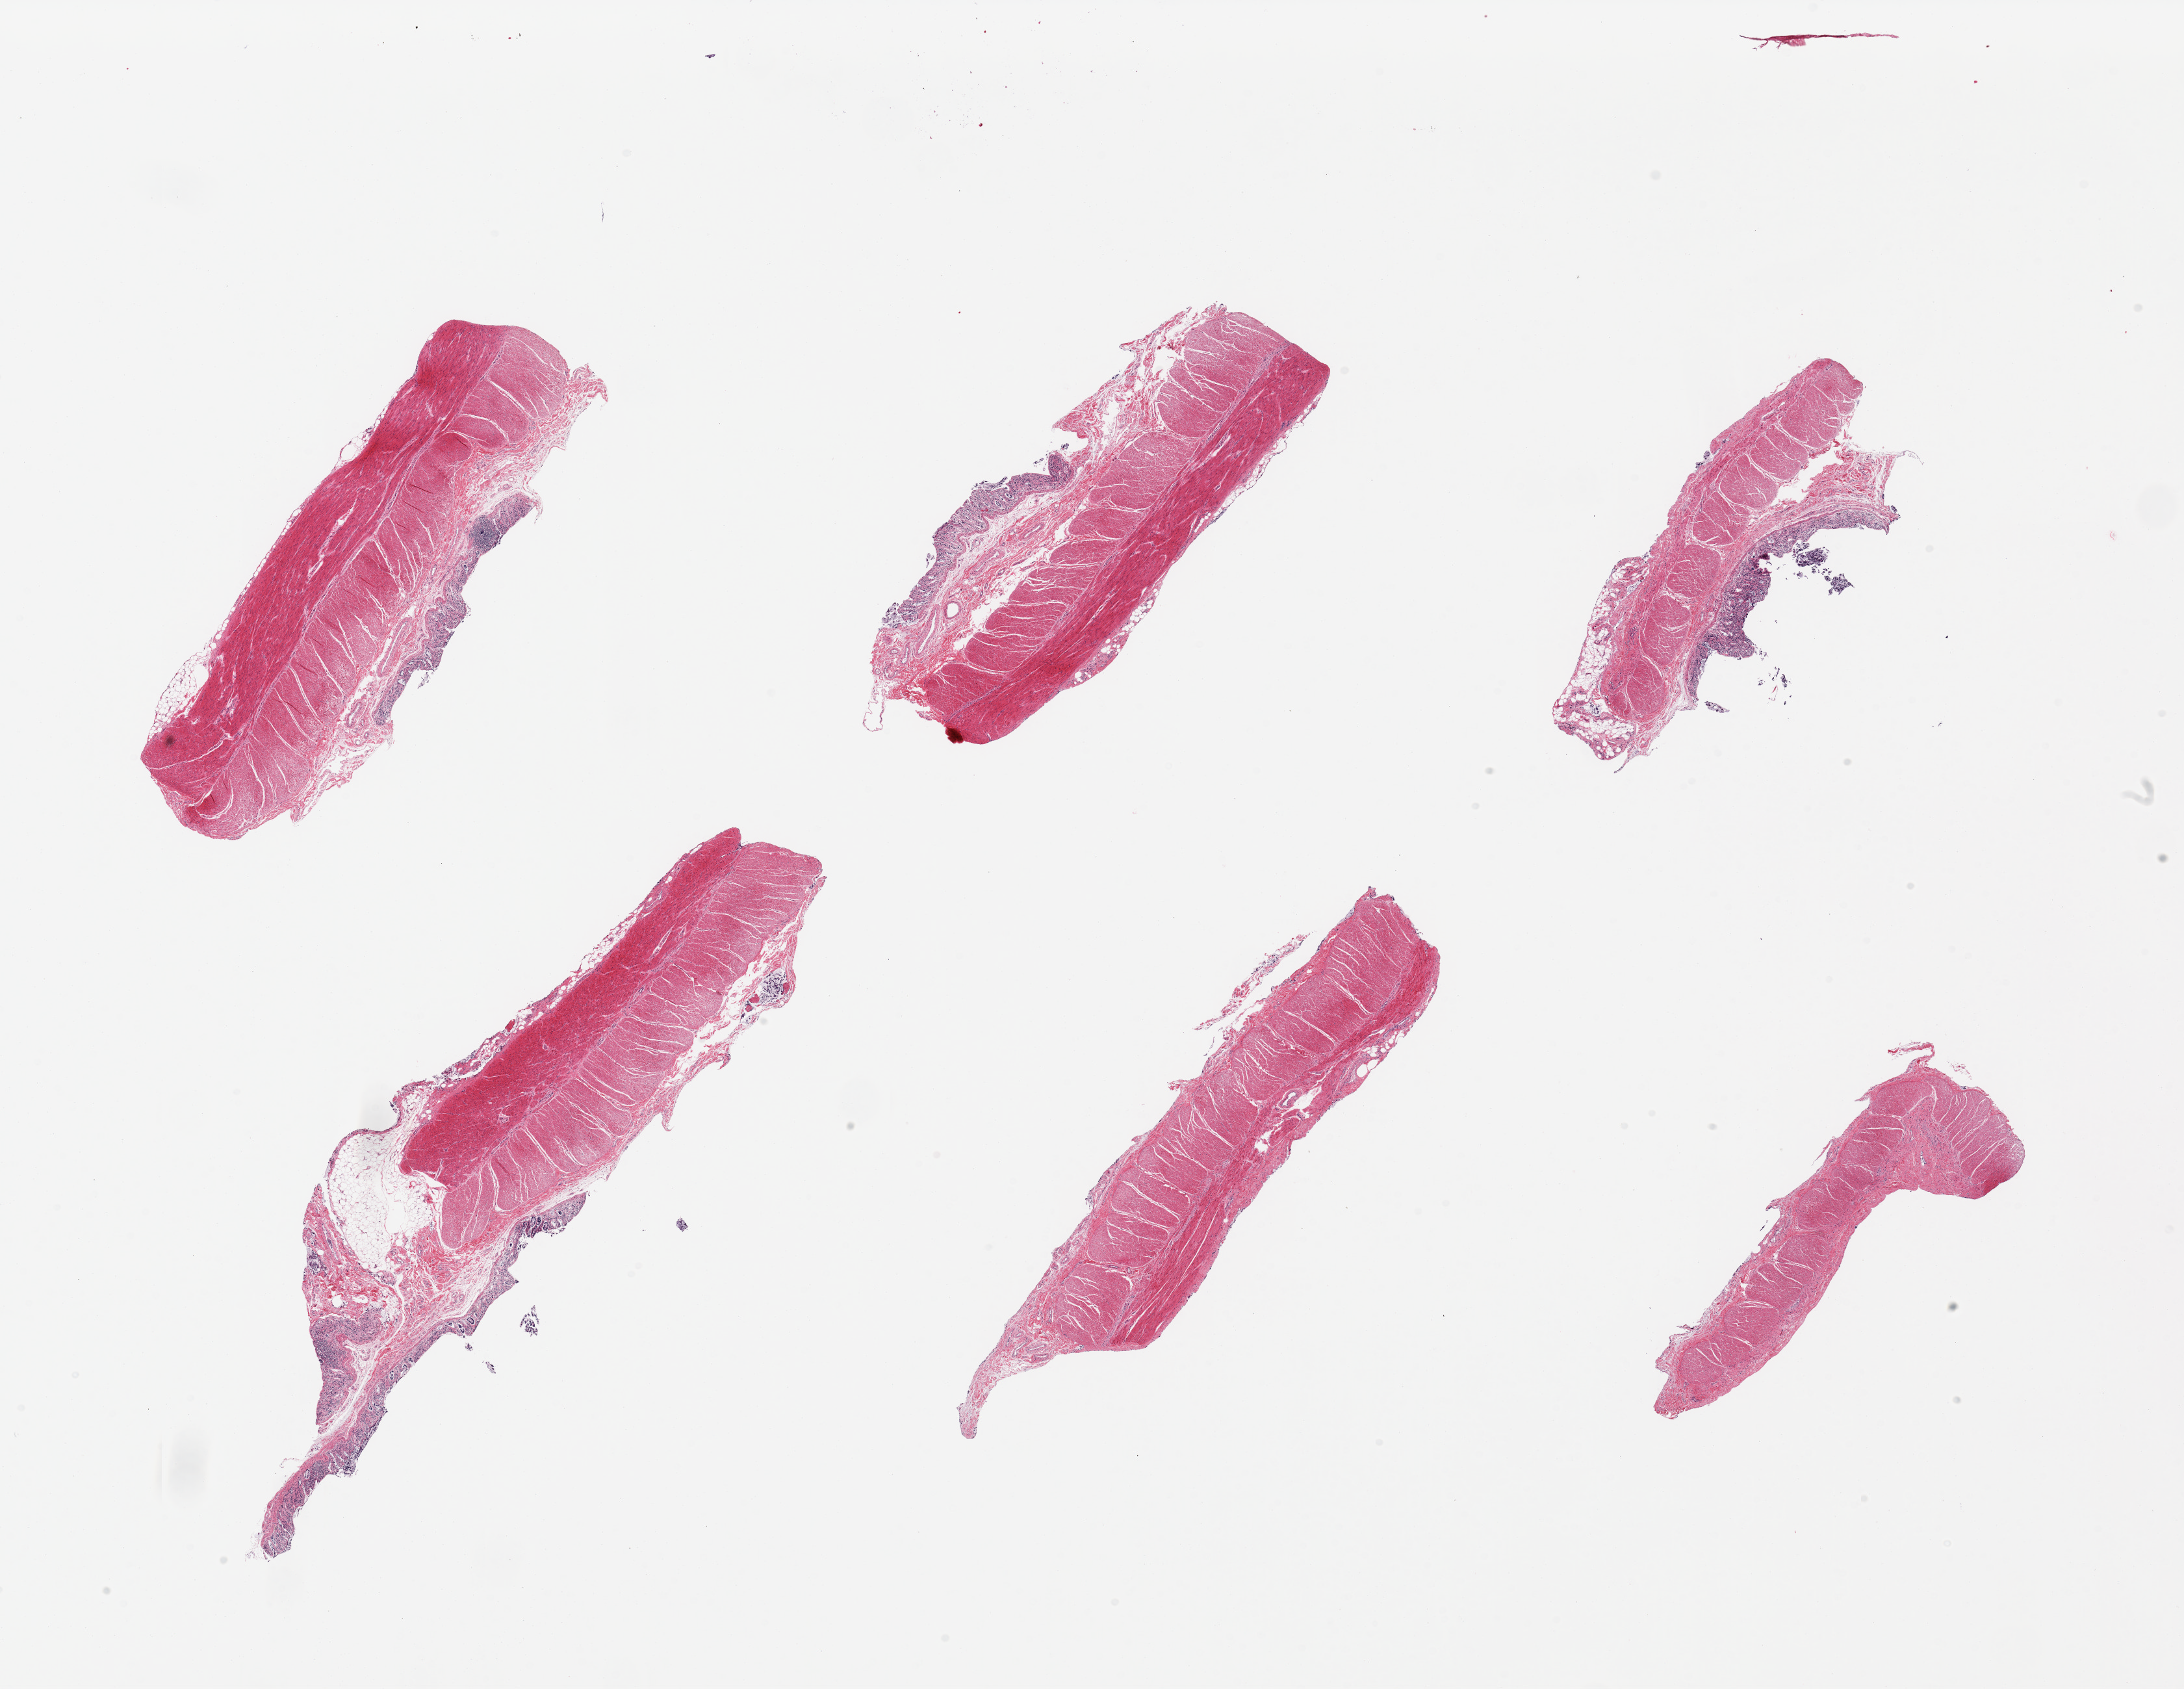
Digitized hematoxylin and eosin (H&E)-stained section, brightfield — whole scanned area (about 26.6 x 20.6 mm, slide scanned at 20x) shown as a low-resolution overview; PAXgene-fixed paraffin-embedded (PFPE) section; sampled site (target tissue): transverse colon; tissue donor sample. Donor: female.
Pathologist's review note for this sample: 6 pieces; mucosa autolyzed (3); muscularis intact.